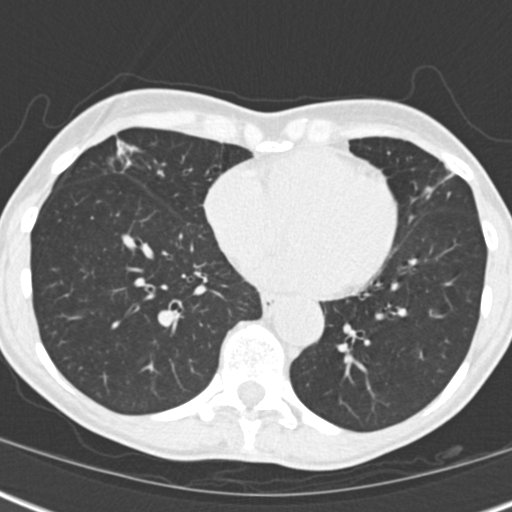
Low-dose screening chest CT, one axial slice. Position 65 of 173 along the scan axis. Reconstruction kernel B30f. 120 kVp. Lung window (W 1500 / L -600 HU). 2 mm slice thickness. 512 × 512 image matrix, field of view 290 × 290 mm.
Annotated regions visible in this slice (outlined manually by an expert reader):
- lesion 1 (tumor, middle lobe of right lung): bounding box [x1, y1, x2, y2] px = [118, 144, 126, 154]